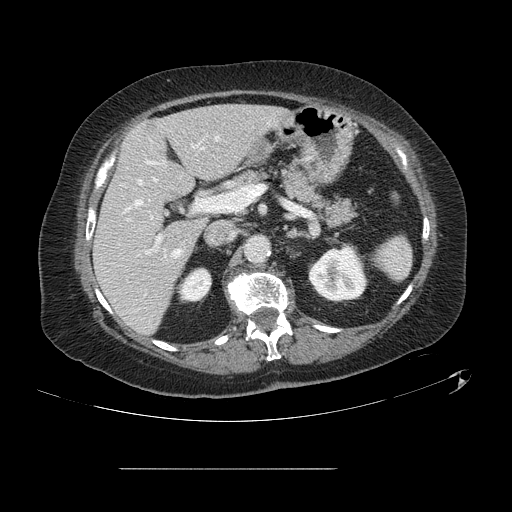
Contrast-enhanced abdominal CT, one axial slice; intravenous contrast given; soft-tissue window (W 400 / L 40 HU); 512 × 512 image matrix, field of view 439 × 439 mm. Female patient, age 75 years. Case-level facts recorded for this patient, not image findings: diagnosis: colorectal cancer liver metastases, imaged before liver resection; multiple liver metastases: no.
Annotated regions visible in this slice (expert manual segmentation):
- hepatic veins: bounding box [x1, y1, x2, y2] px = [125, 137, 218, 257]
- liver: [95, 105, 286, 333]
- planned liver remnant (the part of the liver to remain after resection): [95, 105, 286, 333]
- portal vein (with intrahepatic branches): [144, 146, 209, 254]